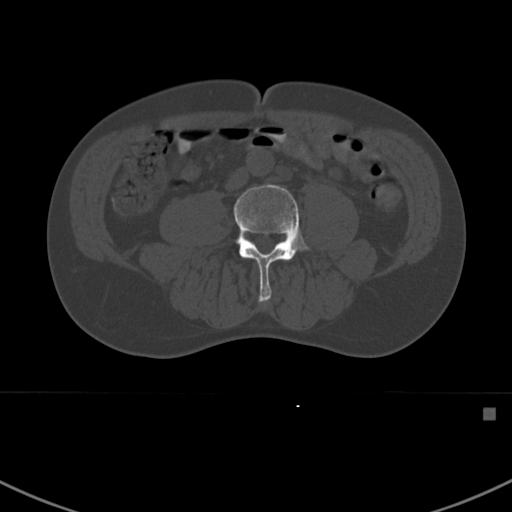
CT including the spine, one axial slice. Slice 241 of 412 in the series (ordered by position). 120 kVp. Bone window (W 1800 / L 400 HU). 1.5 mm slice thickness. 512 × 512 image matrix, field of view 358 × 358 mm. Male patient, age 59 years. Case-level facts recorded for this patient, not image findings: primary cancer: prostate.
Outlined on this slice (semi-automatic segmentation, software-assisted and operator-edited):
- L4 vertebra: bounding box [x1, y1, x2, y2] px = [234, 184, 311, 303]